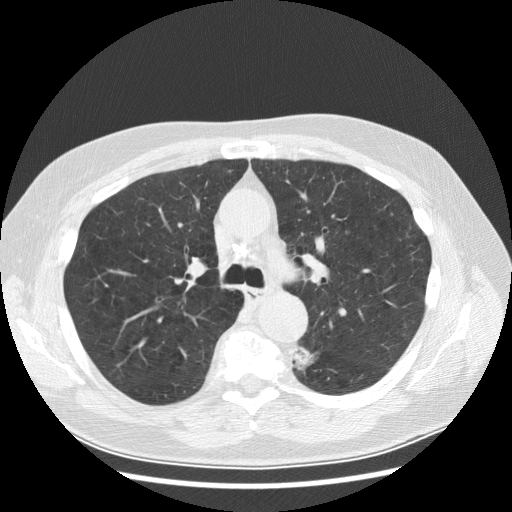
Low-dose screening chest CT, axial slice. Baseline annual screen. Lung window (W 1500 / L -600 HU). 2.5 mm slice thickness. Standard (soft-tissue) reconstruction kernel (STANDARD). 120 kVp. 512 × 512 image matrix, field of view 370 × 370 mm. Male, age 70 years at enrolment. Current smoker at enrolment.
Expert-annotated lung lesion, bounding box <277,338,325,378> (left, top, right, bottom; pixels). Screening reader's record for this exam (one nodule recorded; not confirmed to be the boxed lesion): non-calcified nodule or mass ≥4 mm, left lower lobe, 27 × 16 mm, spiculated (stellate) margins, soft tissue attenuation, pre-existing on the prior screen: yes; interval growth: yes. Lung cancer was diagnosed 97 days after this screen: papillary adenocarcinoma, NOS, left lower lobe, moderately differentiated (G2), stage IB (AJCC 6th edition), 35 mm at pathology.